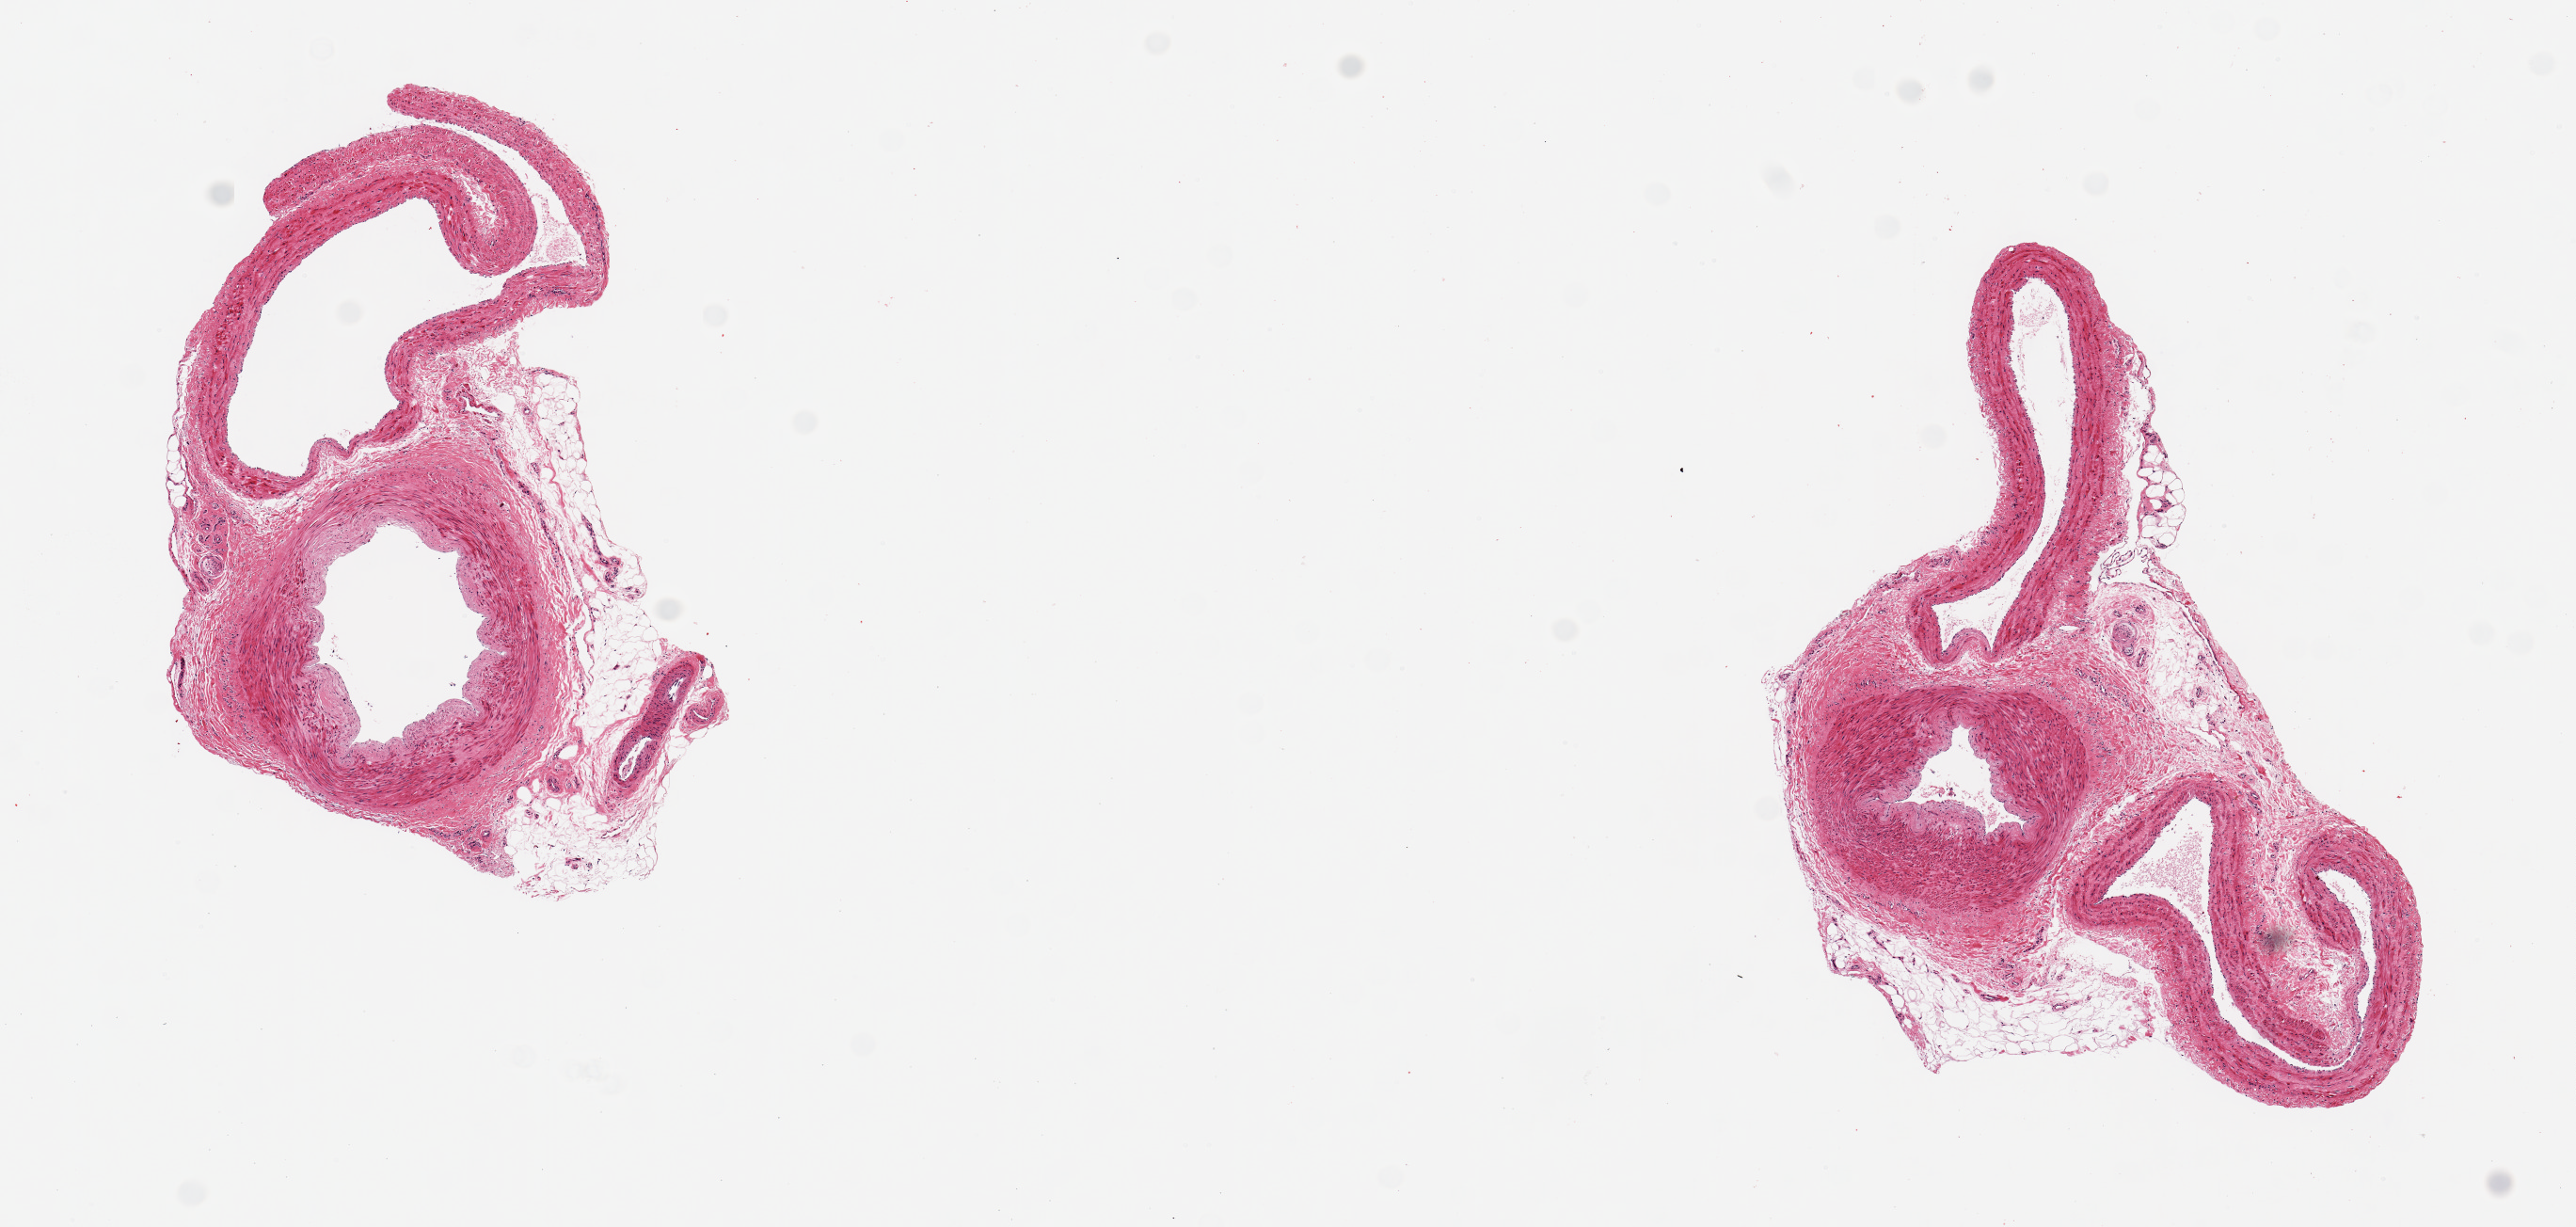
Whole-slide image, haematoxylin and eosin stain — shown as a low-resolution overview of the whole scanned area (about 10.8 x 5.2 mm, acquisition: 20x scan), PAXgene-fixed, paraffin-embedded tissue, section of tibial artery (target tissue), tissue donor sample. Male donor.
Review note (as recorded): 2 pieces ~1mm d; 75% of both aliquots (overall ~4x2mm) are attached vein and adipose tissue.